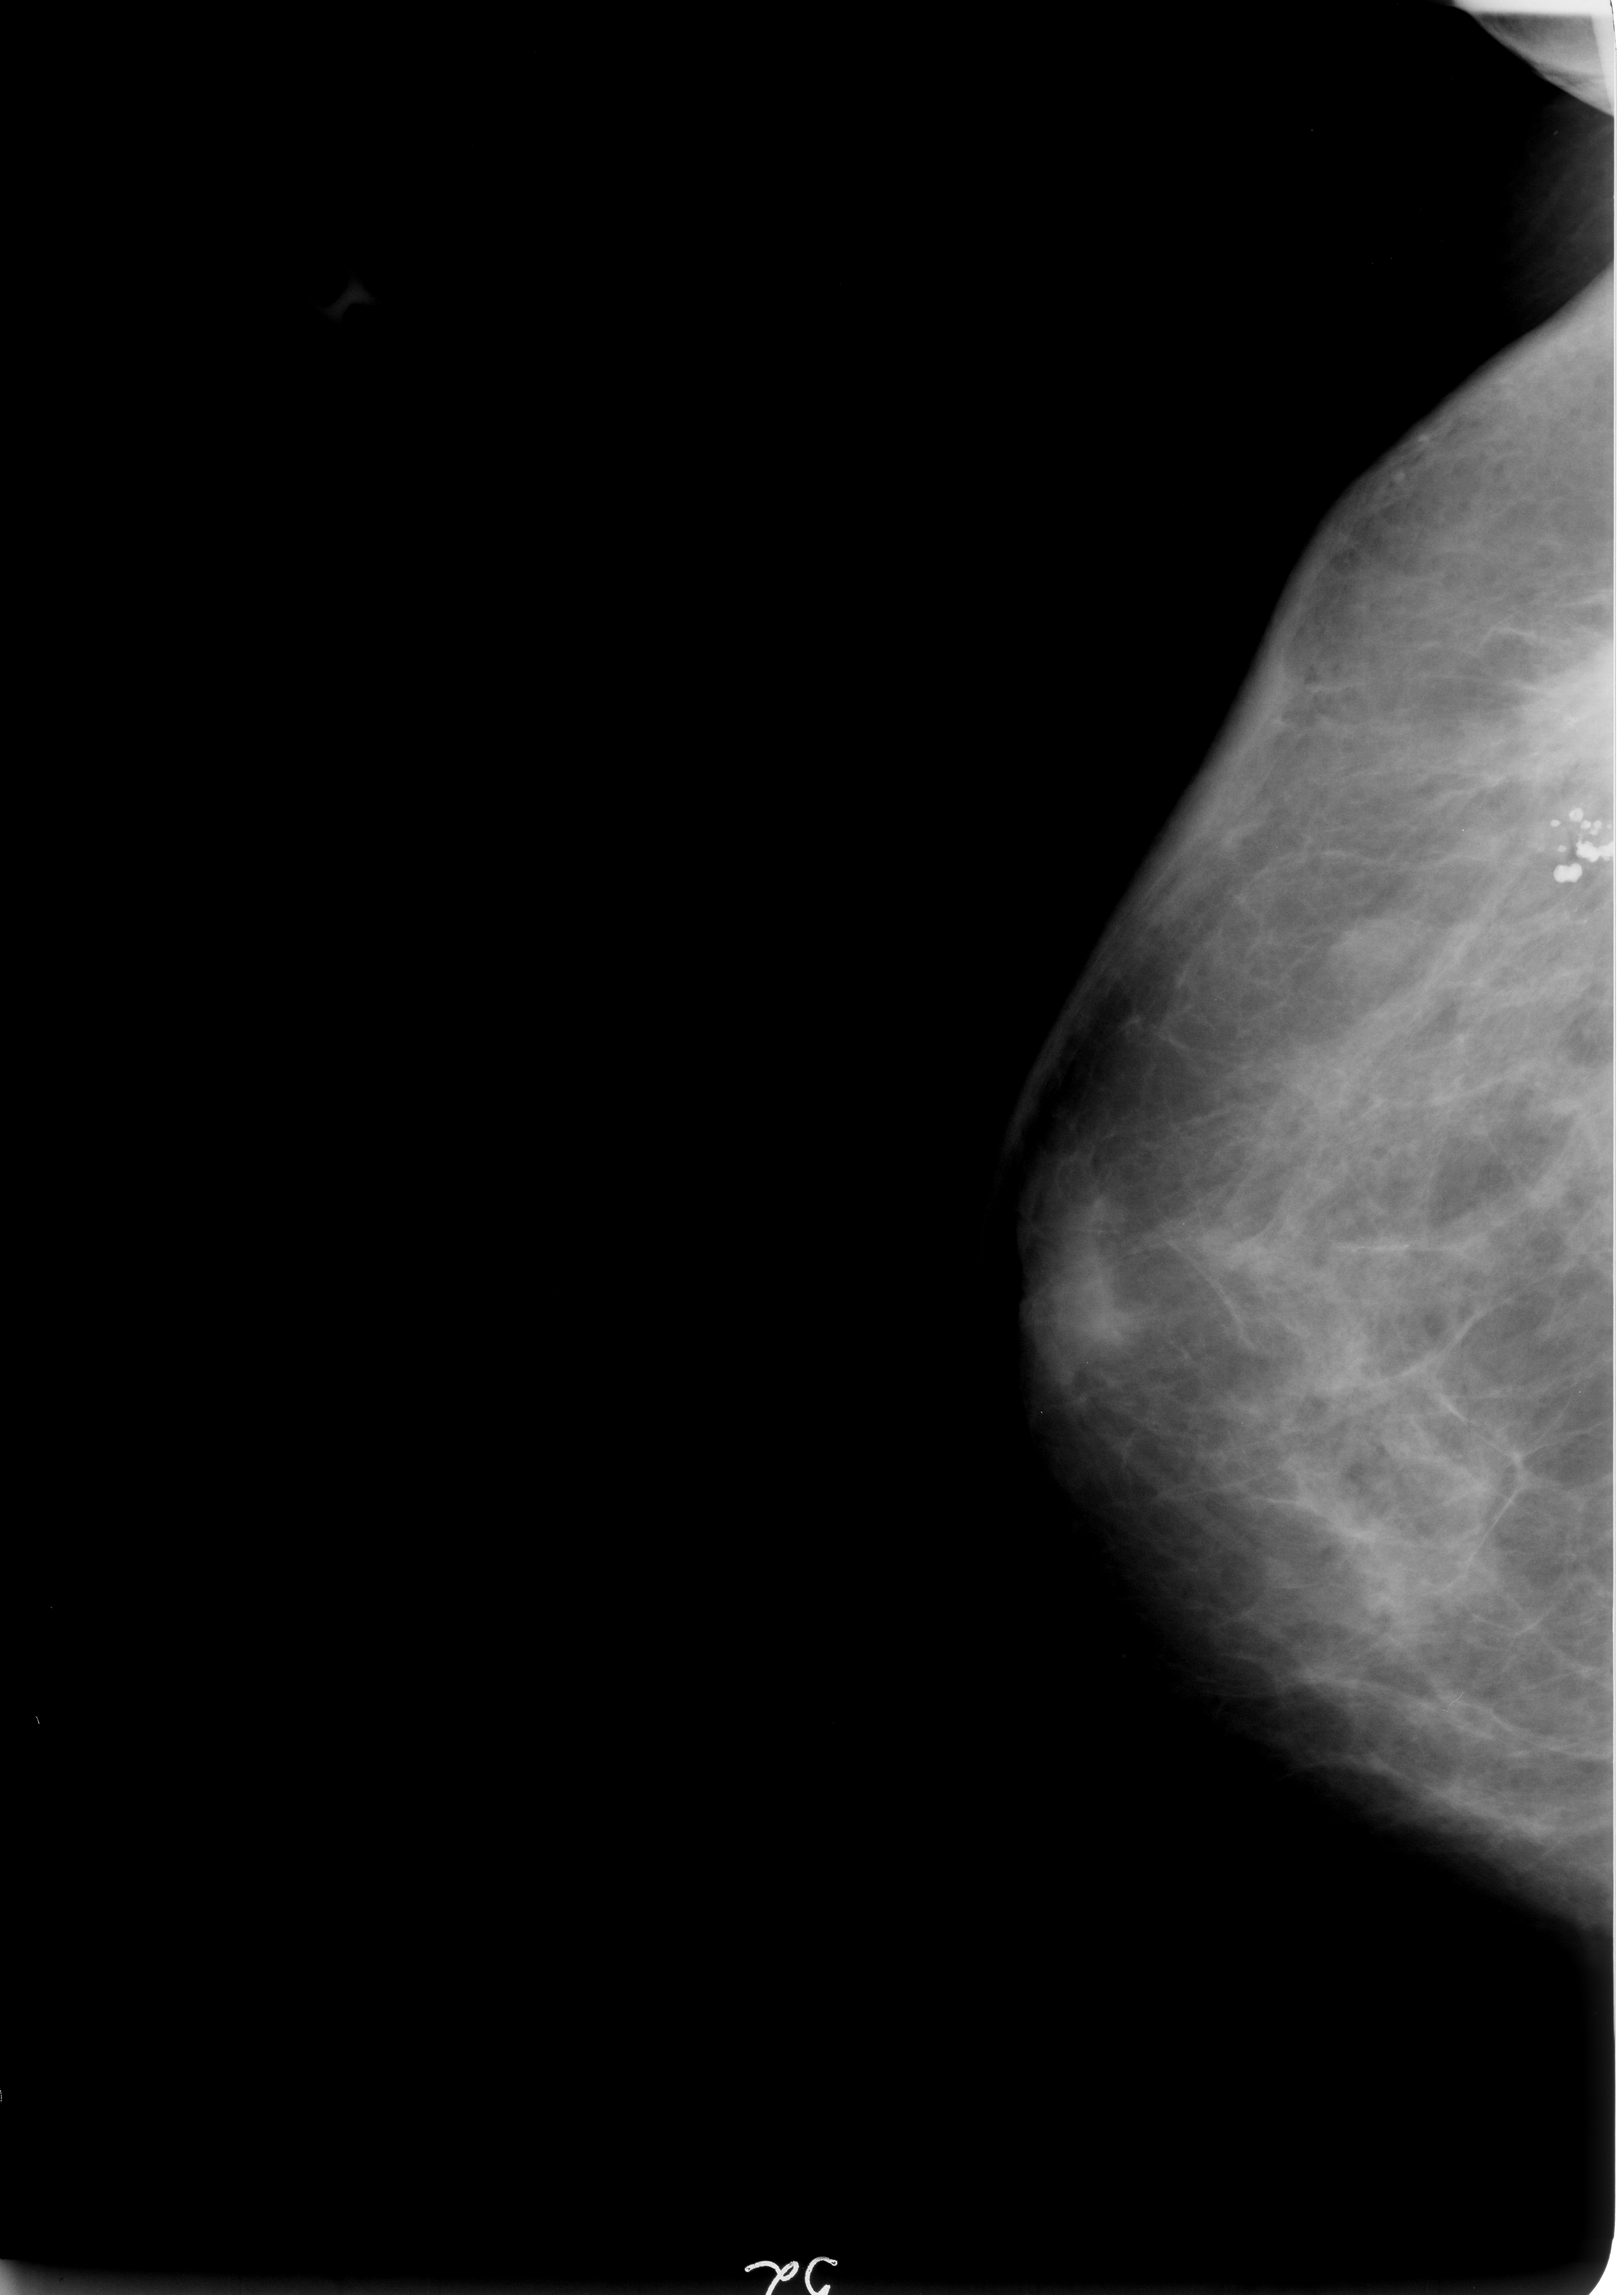
Mammogram (digitized film). Right breast. CC view. 1624 × 2295 image matrix.
Marked abnormalities (boxes around the expert regions of interest):
- Finding 1 of 2: mass, shape irregular / architectural distortion, margins ill defined / spiculated; BI-RADS assessment category 5; subtlety rating 5 on a 1 (subtle) to 5 (obvious) scale; pathology result (as recorded, not read from the image): malignant: bounding box [x1, y1, x2, y2] px = [1179, 630, 1295, 854]
- Finding 2 of 2: mass, shape irregular / architectural distortion, margins ill defined / spiculated; BI-RADS assessment category 5; subtlety rating 5 on a 1 (subtle) to 5 (obvious) scale; pathology result (as recorded, not read from the image): malignant: [1472, 619, 1624, 854]